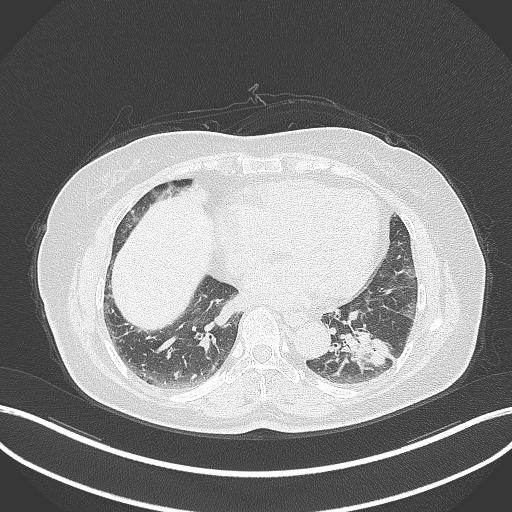
Chest CT, one axial slice. Slice 140 of 311 in the series (ordered by position). Lung window (W 1500 / L -600 HU). 512 × 512 image matrix, field of view 400 × 400 mm. Female patient, age 59 years. From the clinical record (not read from this slice): clinical TNM (as recorded): T2a N0 M0; histopathological grade: G2-3.
Annotated regions visible in this slice (bounding box drawn by a radiologist):
- lung tumour (recorded histology: adenocarcinoma): bounding box [x1, y1, x2, y2] px = [342, 323, 393, 374]